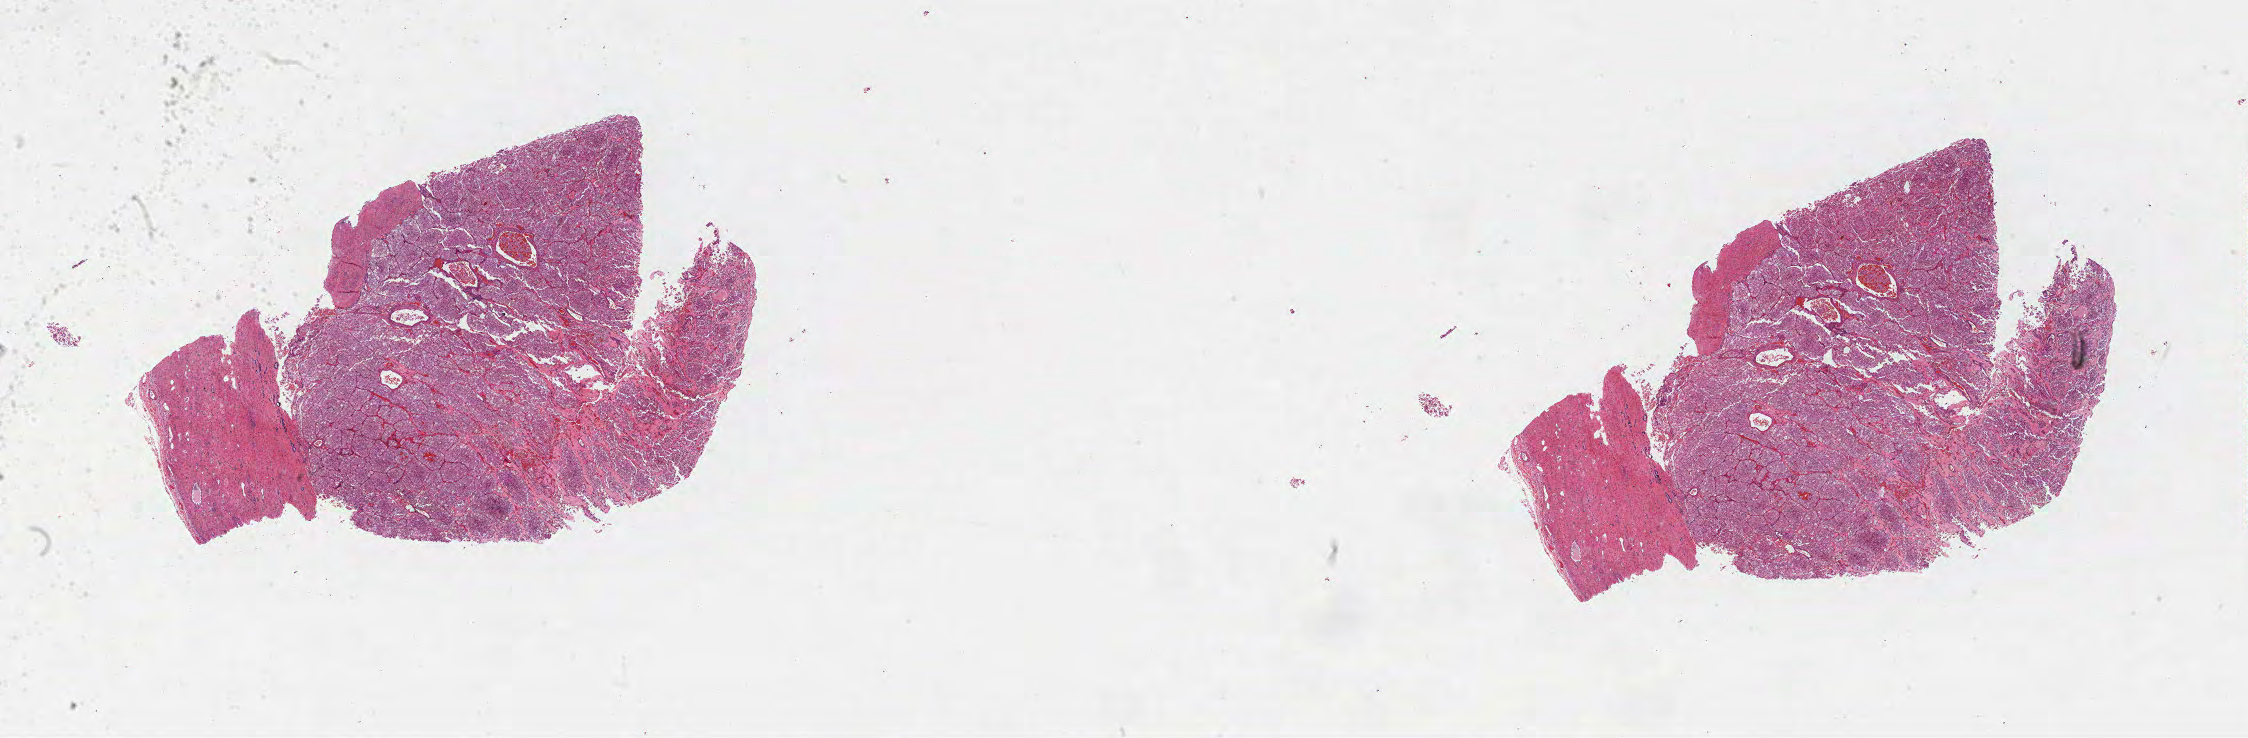
H&E-stained whole-slide image, low-resolution overview of the scanned area, about 36.3 x 11.9 mm (slide scanned at 40x); formalin-fixed paraffin-embedded (FFPE) diagnostic section; primary tumour sample from the kidney. Male, age 59 years at initial diagnosis. Histologic grade: G2 (moderately differentiated).
- histologic diagnosis: Clear cell adenocarcinoma, NOS
- AJCC pathologic stage: II